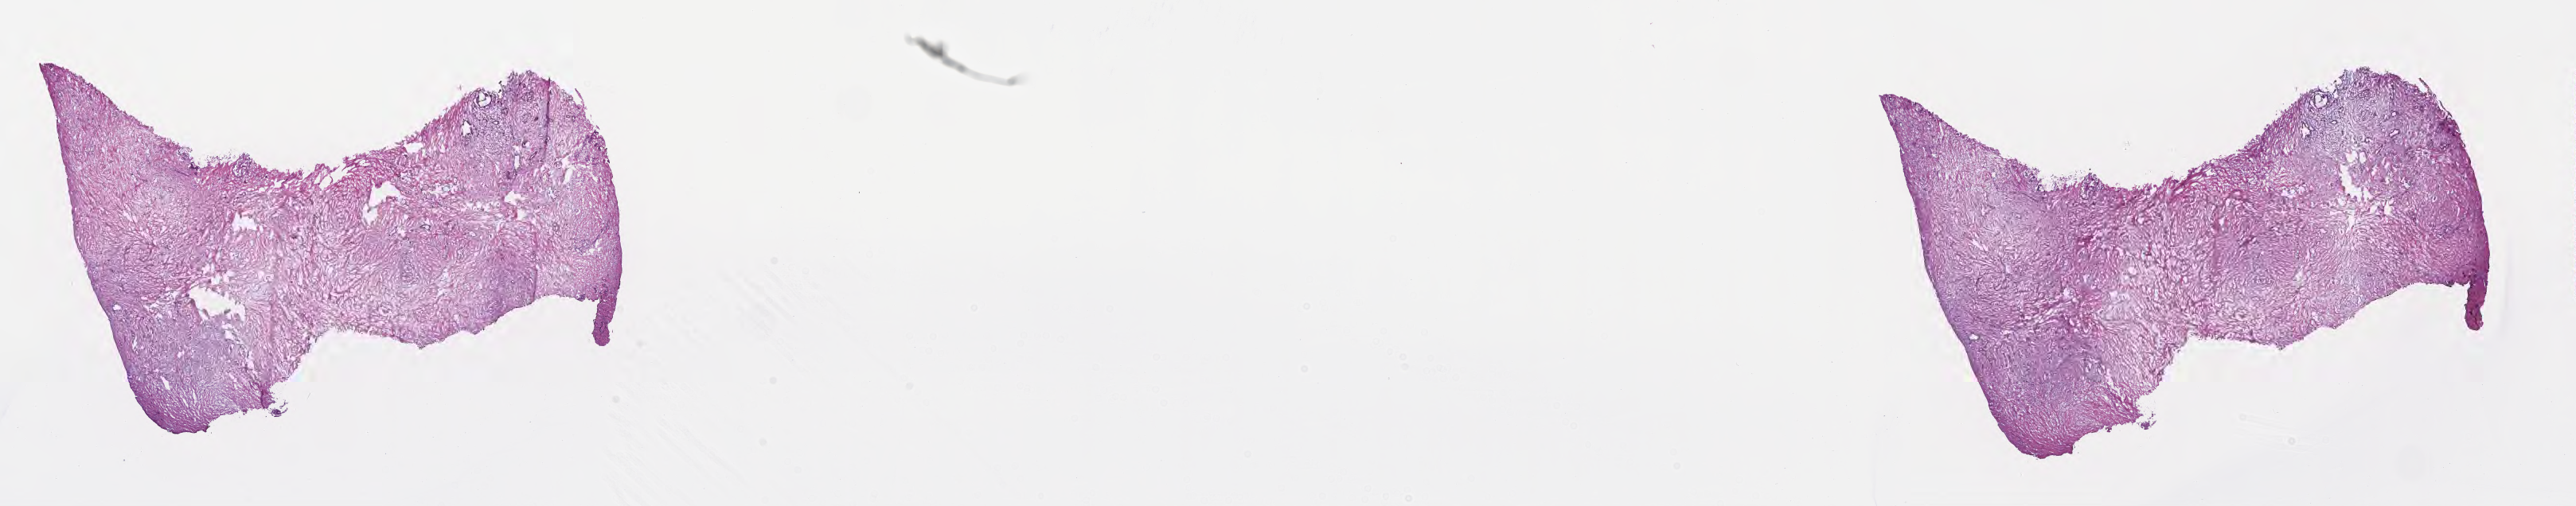
Digitized H&E-stained section, whole scanned area (about 26.2 x 5.1 mm) shown as a low-resolution overview; frozen section; primary tumor; anatomic site: tail of pancreas. Patient: female, age at initial diagnosis 70 years. Composition of this section per pathologist review: tumor cells 3%, tumor nuclei 5%, stromal cells 79%, necrosis 18%, normal cells 0%. Inflammatory infiltration, as recorded: lymphocyte infiltration 12%, monocyte infiltration 2%, neutrophil infiltration 0%.
Diagnosis: Infiltrating duct carcinoma, NOS.